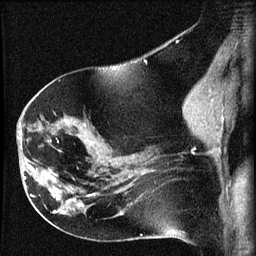
Breast MRI (dynamic contrast-enhanced), one sagittal slice; position 36 of 60 along the scan axis; dynamic contrast-enhanced series, image 2 of 3 at this slice position (ordered by acquisition); 1.5 T; TE 4.2 ms, TR 8.2 ms; 256 × 256 image matrix, field of view 180 × 180 mm. Female patient, age 63 years.
Structures marked on this image (semi-automatic segmentation, software-assisted and operator-edited):
- analysis volume of interest (the breast-tissue region the enhancement analysis was run in; not a lesion): bounding box <22,156,64,202> (left, top, right, bottom; pixels)
- tumour enhancement mask (voxels above the 70 % enhancement threshold inside the analysis volume of interest): <24,164,59,199>